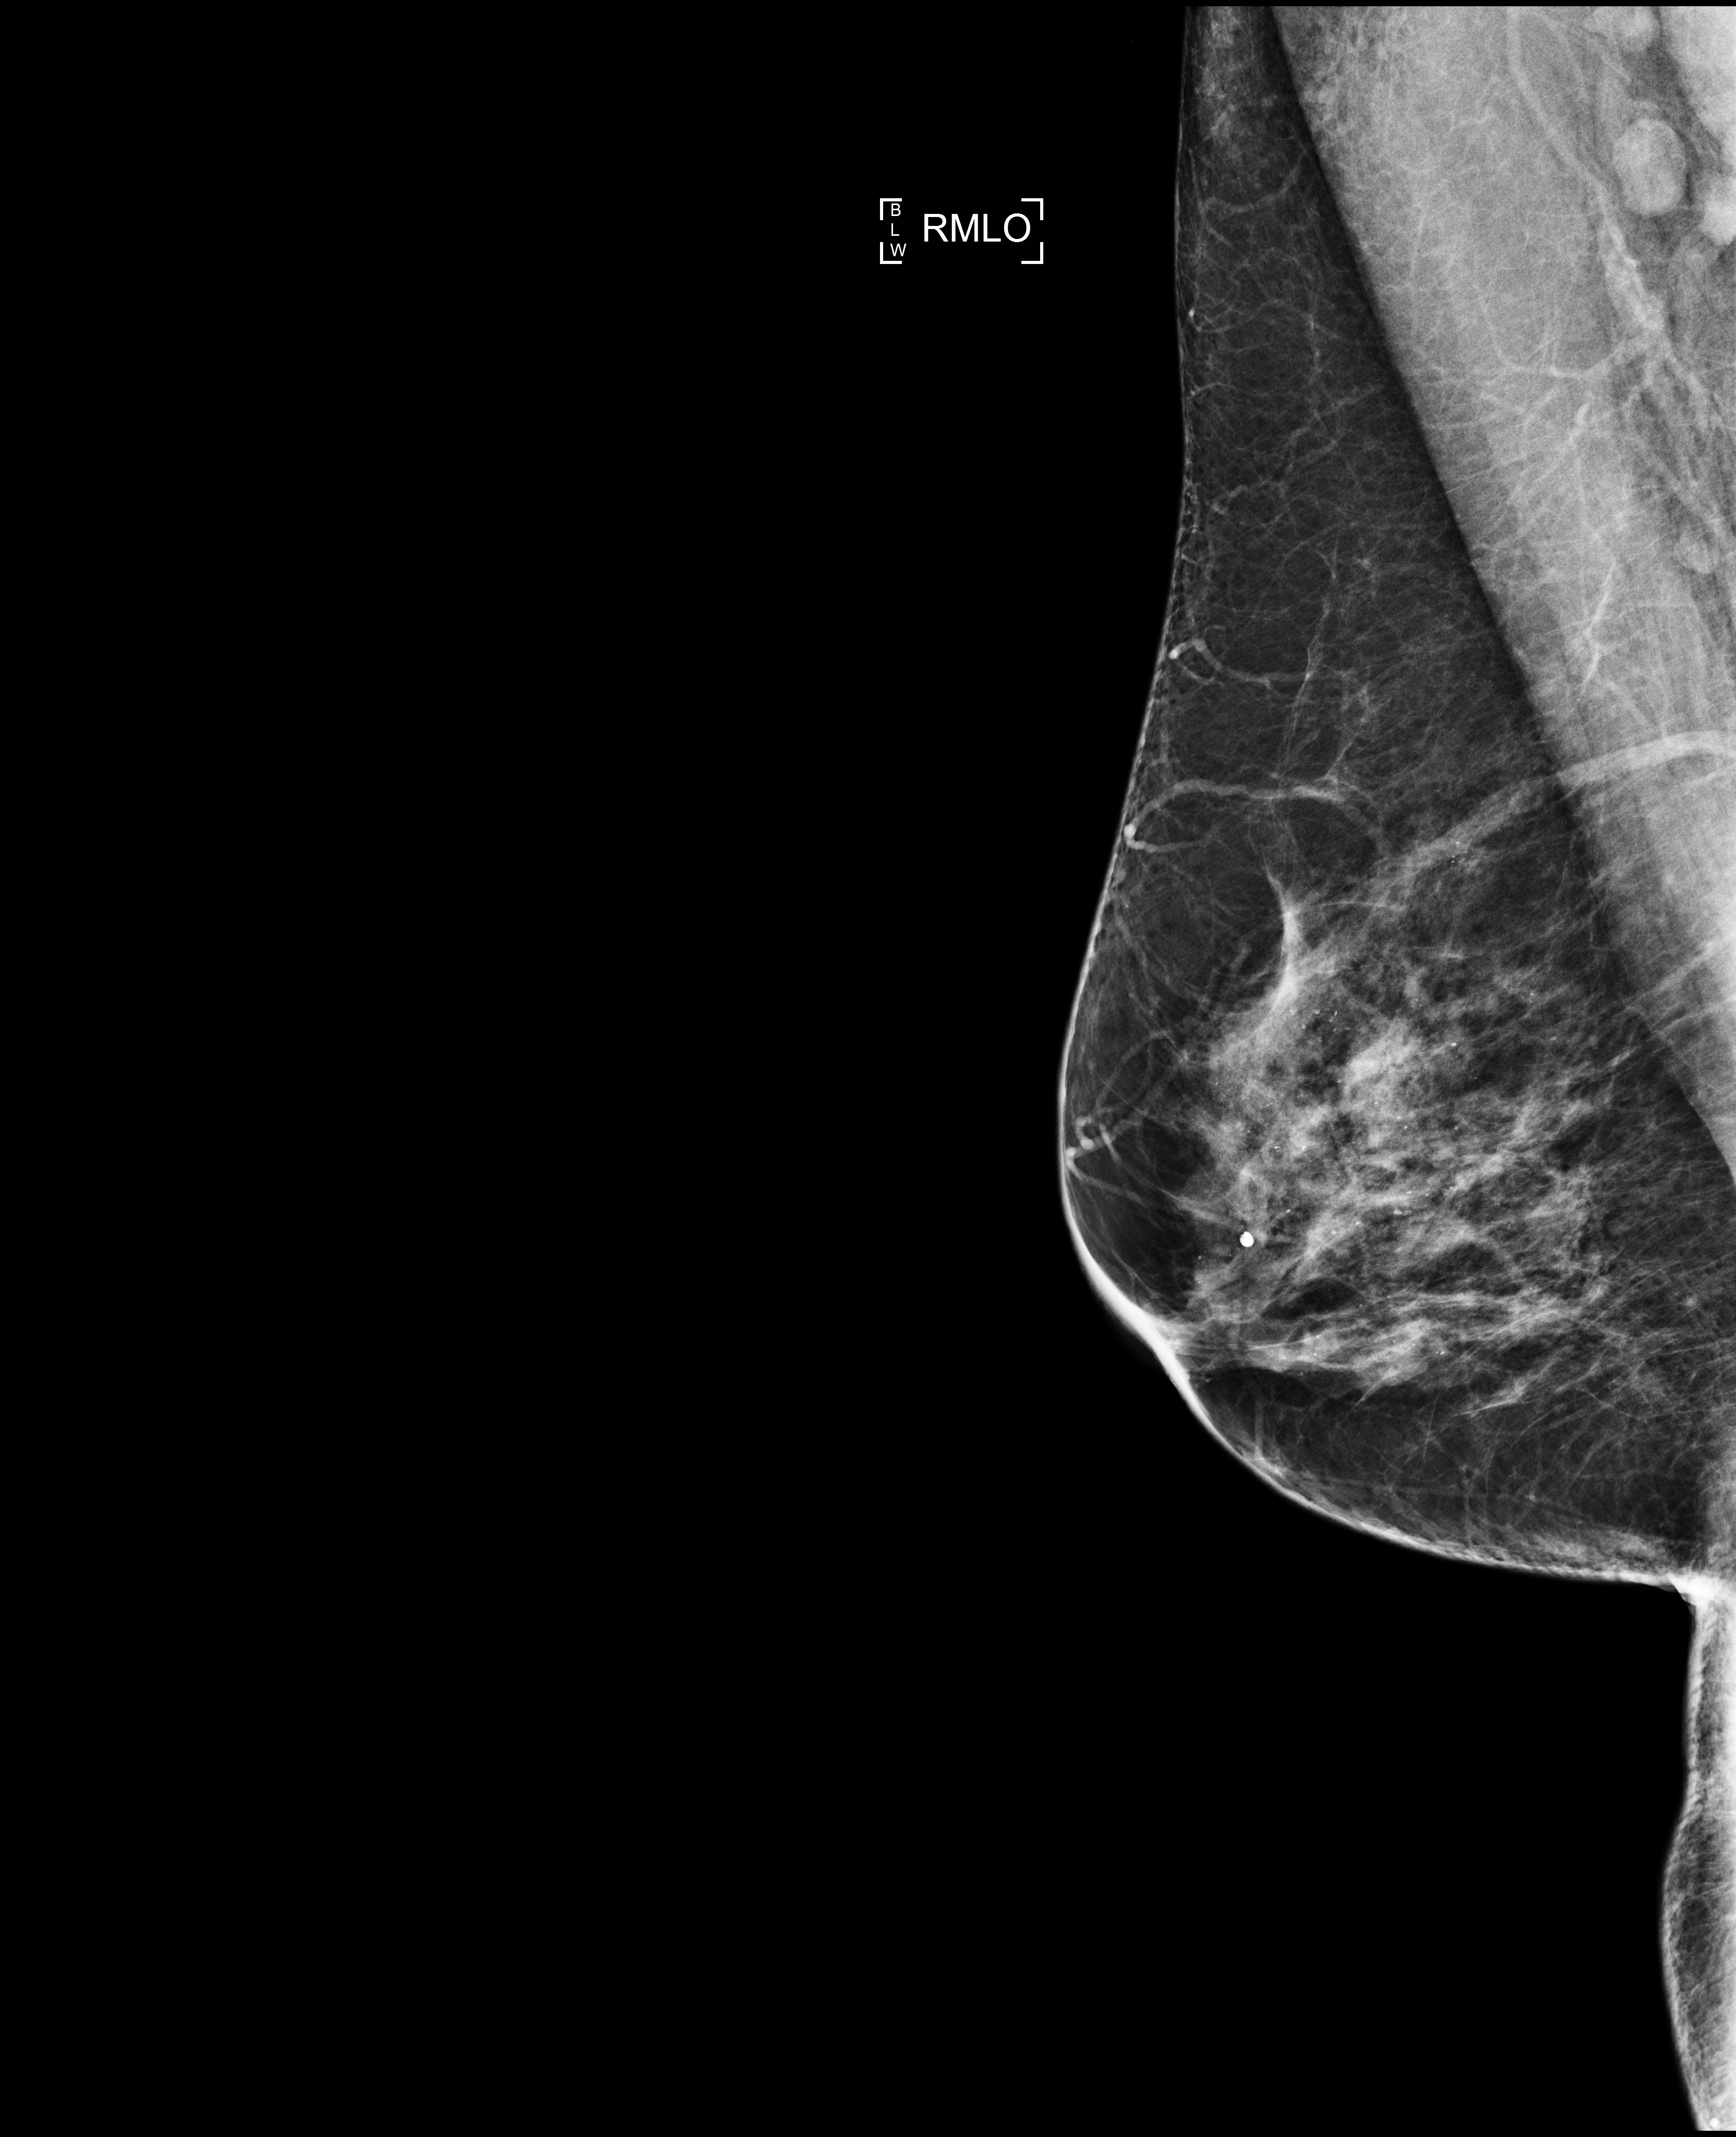
Digital mammogram (FFDM); right breast; MLO view; annual screening mammography examination. Patient aged 50 years (female).
Final BI-RADS assessment for this screening round (tomosynthesis exam, both breasts): category 2.